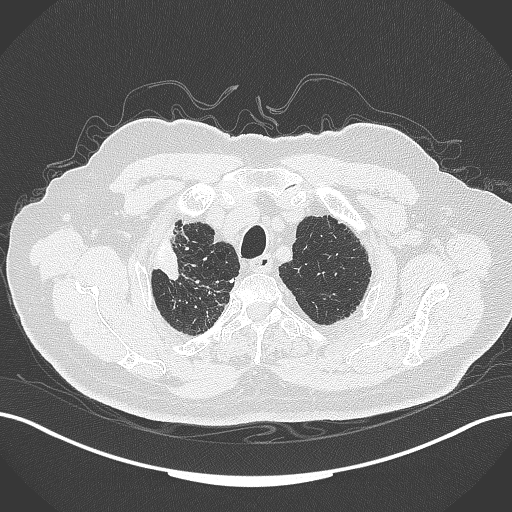
Chest CT, one axial slice. Slice 311 of 389 in the series (ordered by position). Reconstruction kernel B70f. Lung window (W 1500 / L -600 HU). 1 mm slice thickness. 512 × 512 image matrix, field of view 400 × 400 mm. Male patient, age 72 years. From the clinical record (not read from this slice): clinical TNM (as recorded): T1a N0 M0.
Annotated regions visible in this slice (bounding box drawn by a radiologist):
- lung tumour (recorded histology: squamous cell carcinoma): bounding box (x1, y1, x2, y2) in pixels: (153, 230, 184, 278)